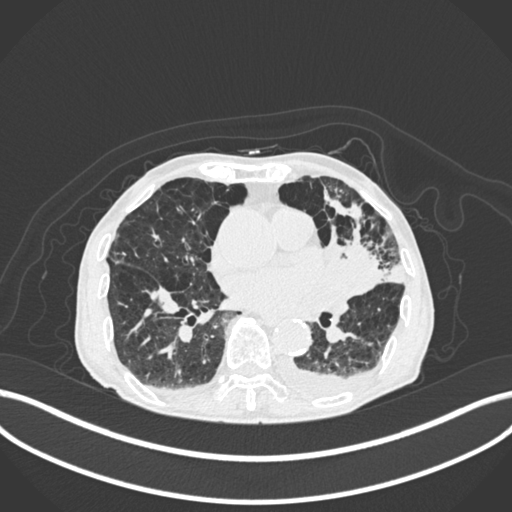
Chest CT, one axial slice. Slice 95 of 400 in the series (ordered by position). 120 kVp. Lung window (W 1500 / L -600 HU). 1 mm slice thickness. 512 × 512 image matrix, field of view 400 × 400 mm. Male patient, age 90 years or older. Case-level facts recorded for this patient, not image findings: clinical TNM (as recorded): T2b N1 M0.
Structures marked on this image (bounding box drawn by a radiologist):
- lung tumour (recorded histology: squamous cell carcinoma): bounding box (x1, y1, x2, y2) in pixels: (325, 234, 385, 305)